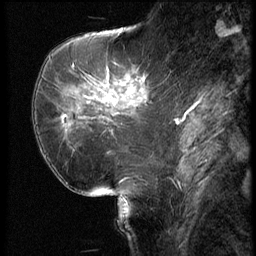
Breast MRI (dynamic contrast-enhanced), one sagittal slice. Position 24 of 62 along the scan axis. 3 images stored at this slice position (order not interpretable as contrast timing). 1.5 T. TE 4.2 ms, TR 9 ms. 256 × 256 image matrix. Patient: female, 62 years. Case-level facts recorded for this patient, not image findings: setting: breast cancer imaged before/during neoadjuvant chemotherapy; receptor status: HR-positive, HER2-negative.
Structures marked on this image (semi-automatically segmented with operator editing):
- analysis volume of interest (the breast-tissue region the enhancement analysis was run in; not a lesion): box from (x=56, y=62) to (x=154, y=155) px
- tumour enhancement mask (voxels above the 140 % enhancement threshold inside the analysis volume of interest): (x=63, y=90)–(x=133, y=119)